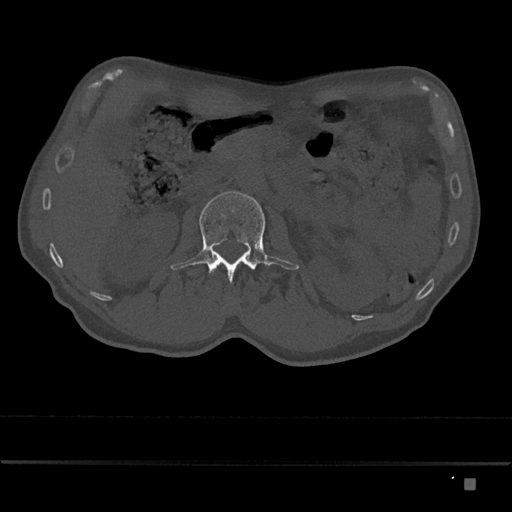
CT including the spine, one axial slice. Slice 482 of 797 in the series (ordered by position). 120 kVp. Bone window (W 1800 / L 400 HU). 0.5 mm slice thickness. 512 × 512 image matrix, field of view 390 × 390 mm. Patient: male, 72 years. From the clinical record (not read from this slice): primary cancer: prostate.
Annotated regions visible in this slice (semi-automatically segmented with operator editing):
- L2 vertebra: box from (x=170, y=191) to (x=299, y=283) px